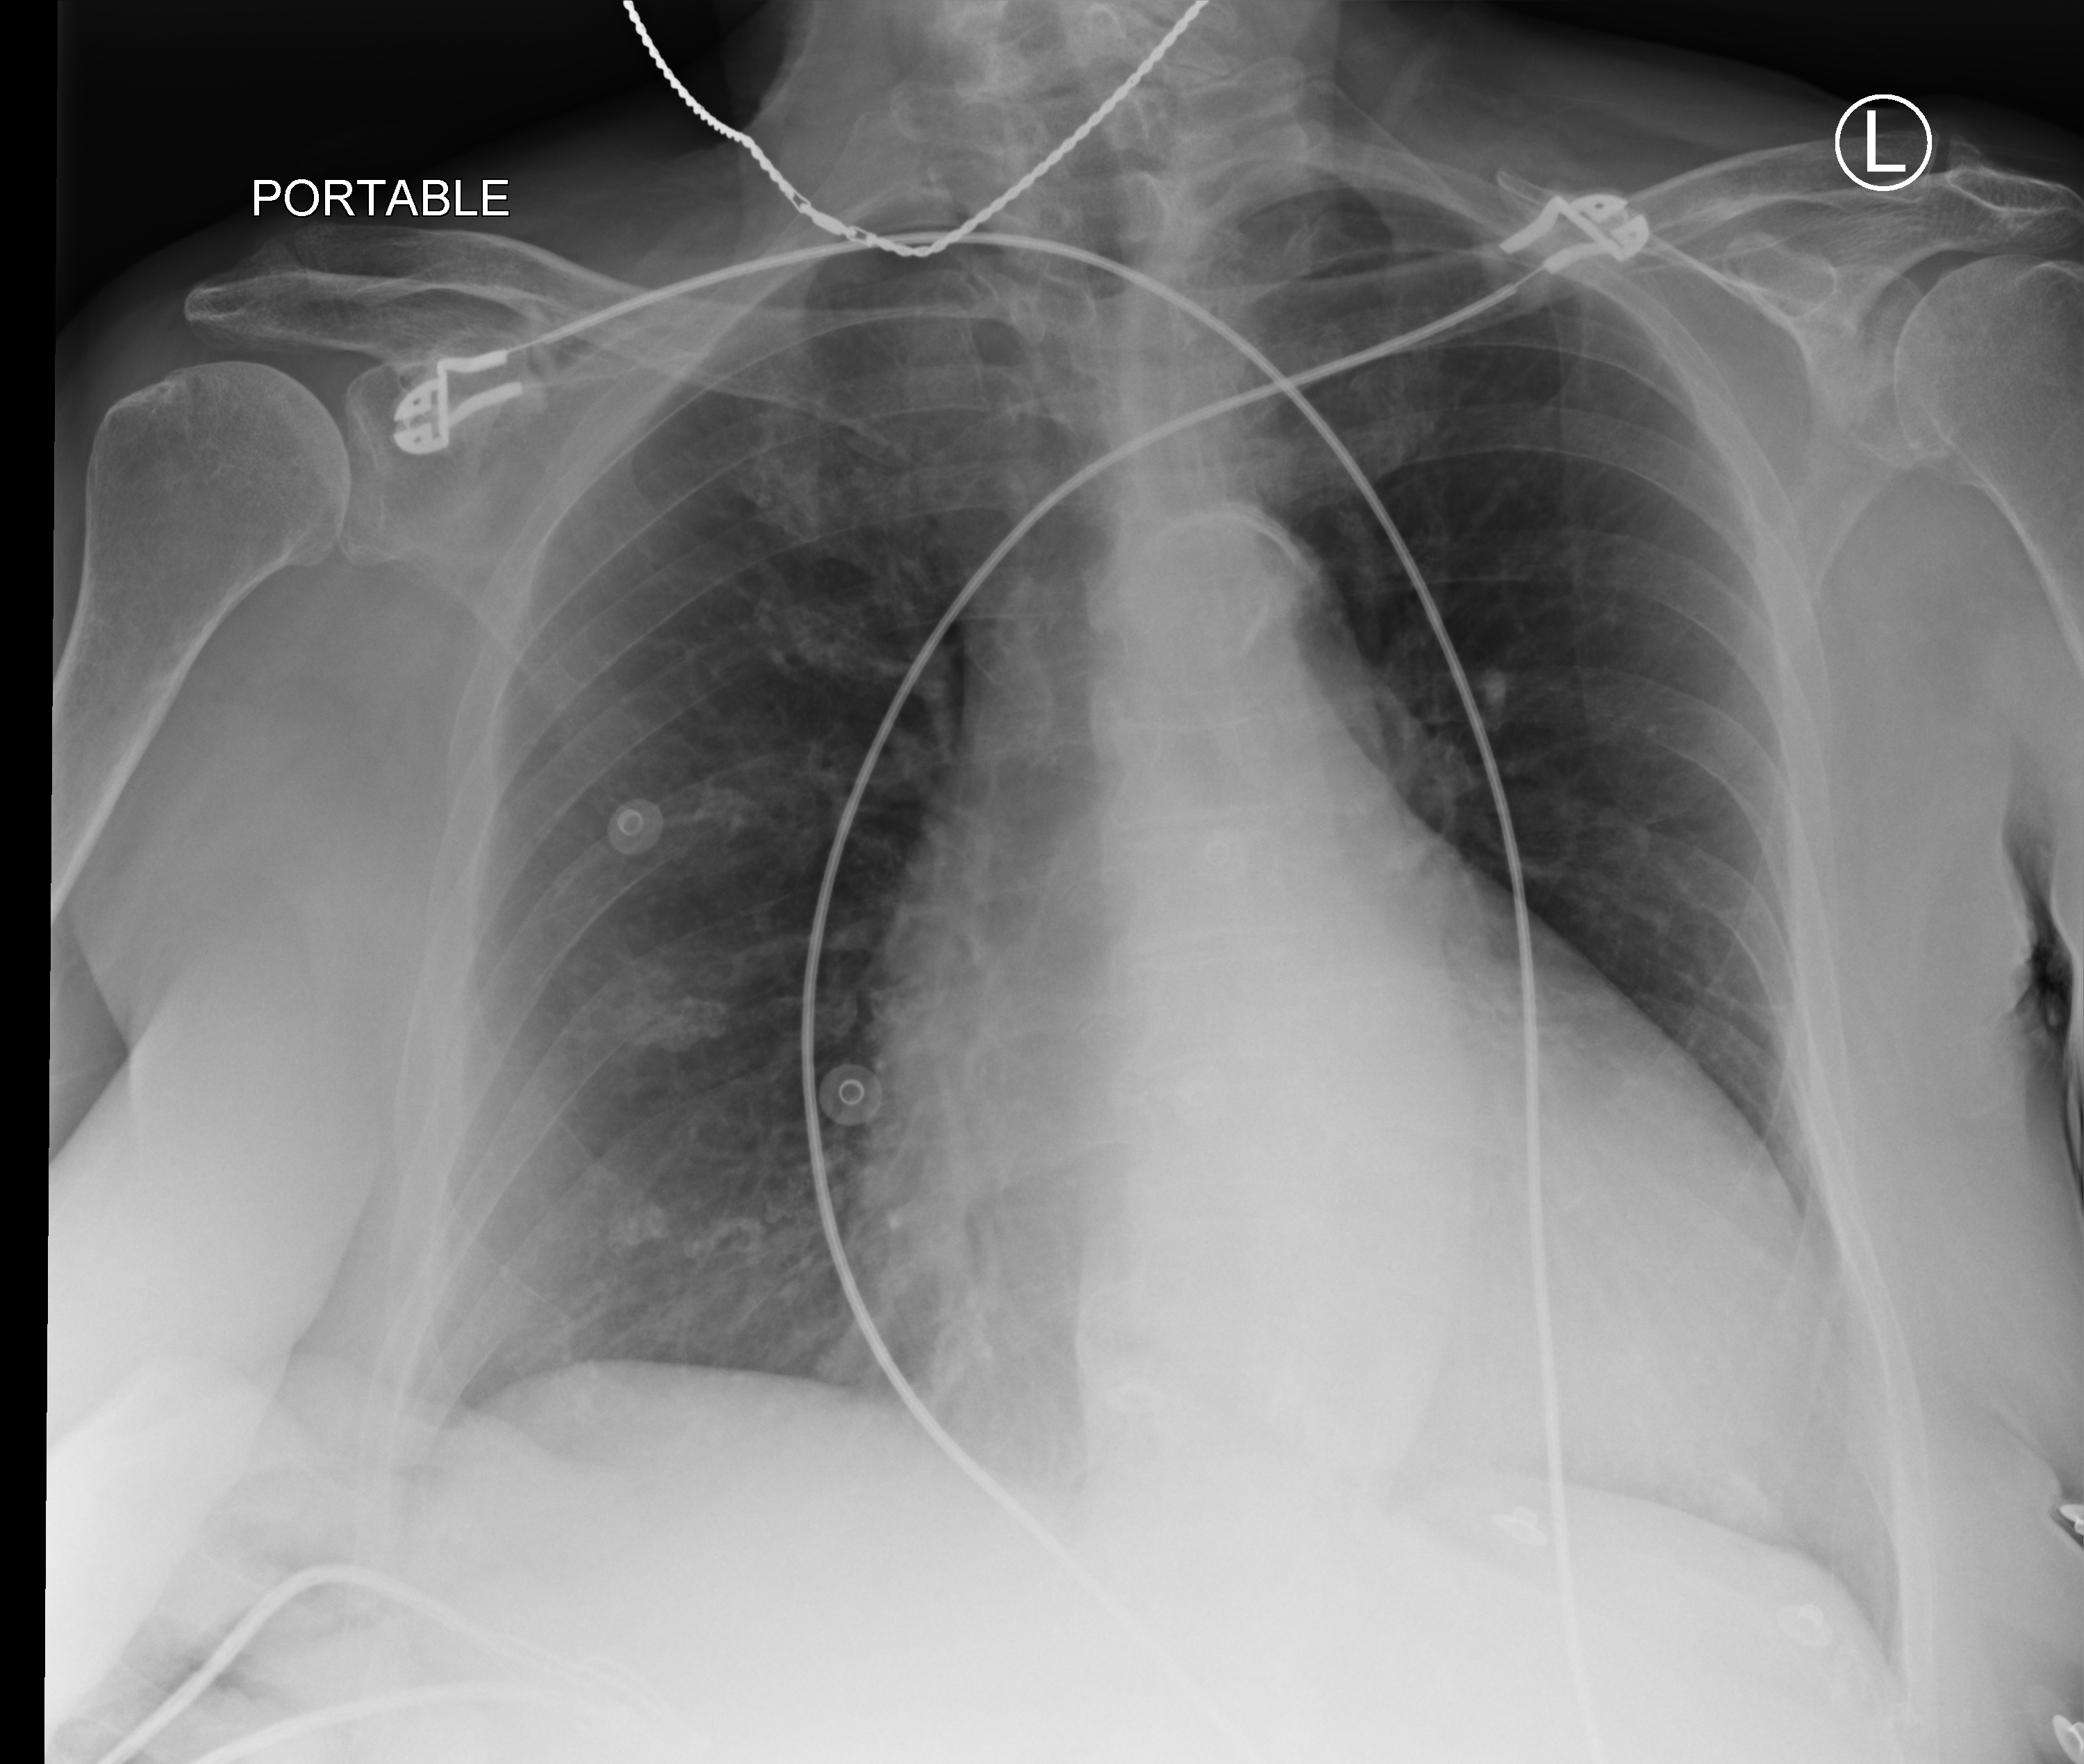
Portable chest radiograph, anteroposterior (AP) projection. Patient hospitalised with COVID-19; female, aged 75–90 years.
Admission-level facts for this patient (not findings on this image; timing relative to this image not recorded):
- COPD (admission record): no
- admitted to intensive care during this hospital stay: no
- other chronic lung disease (admission record): no